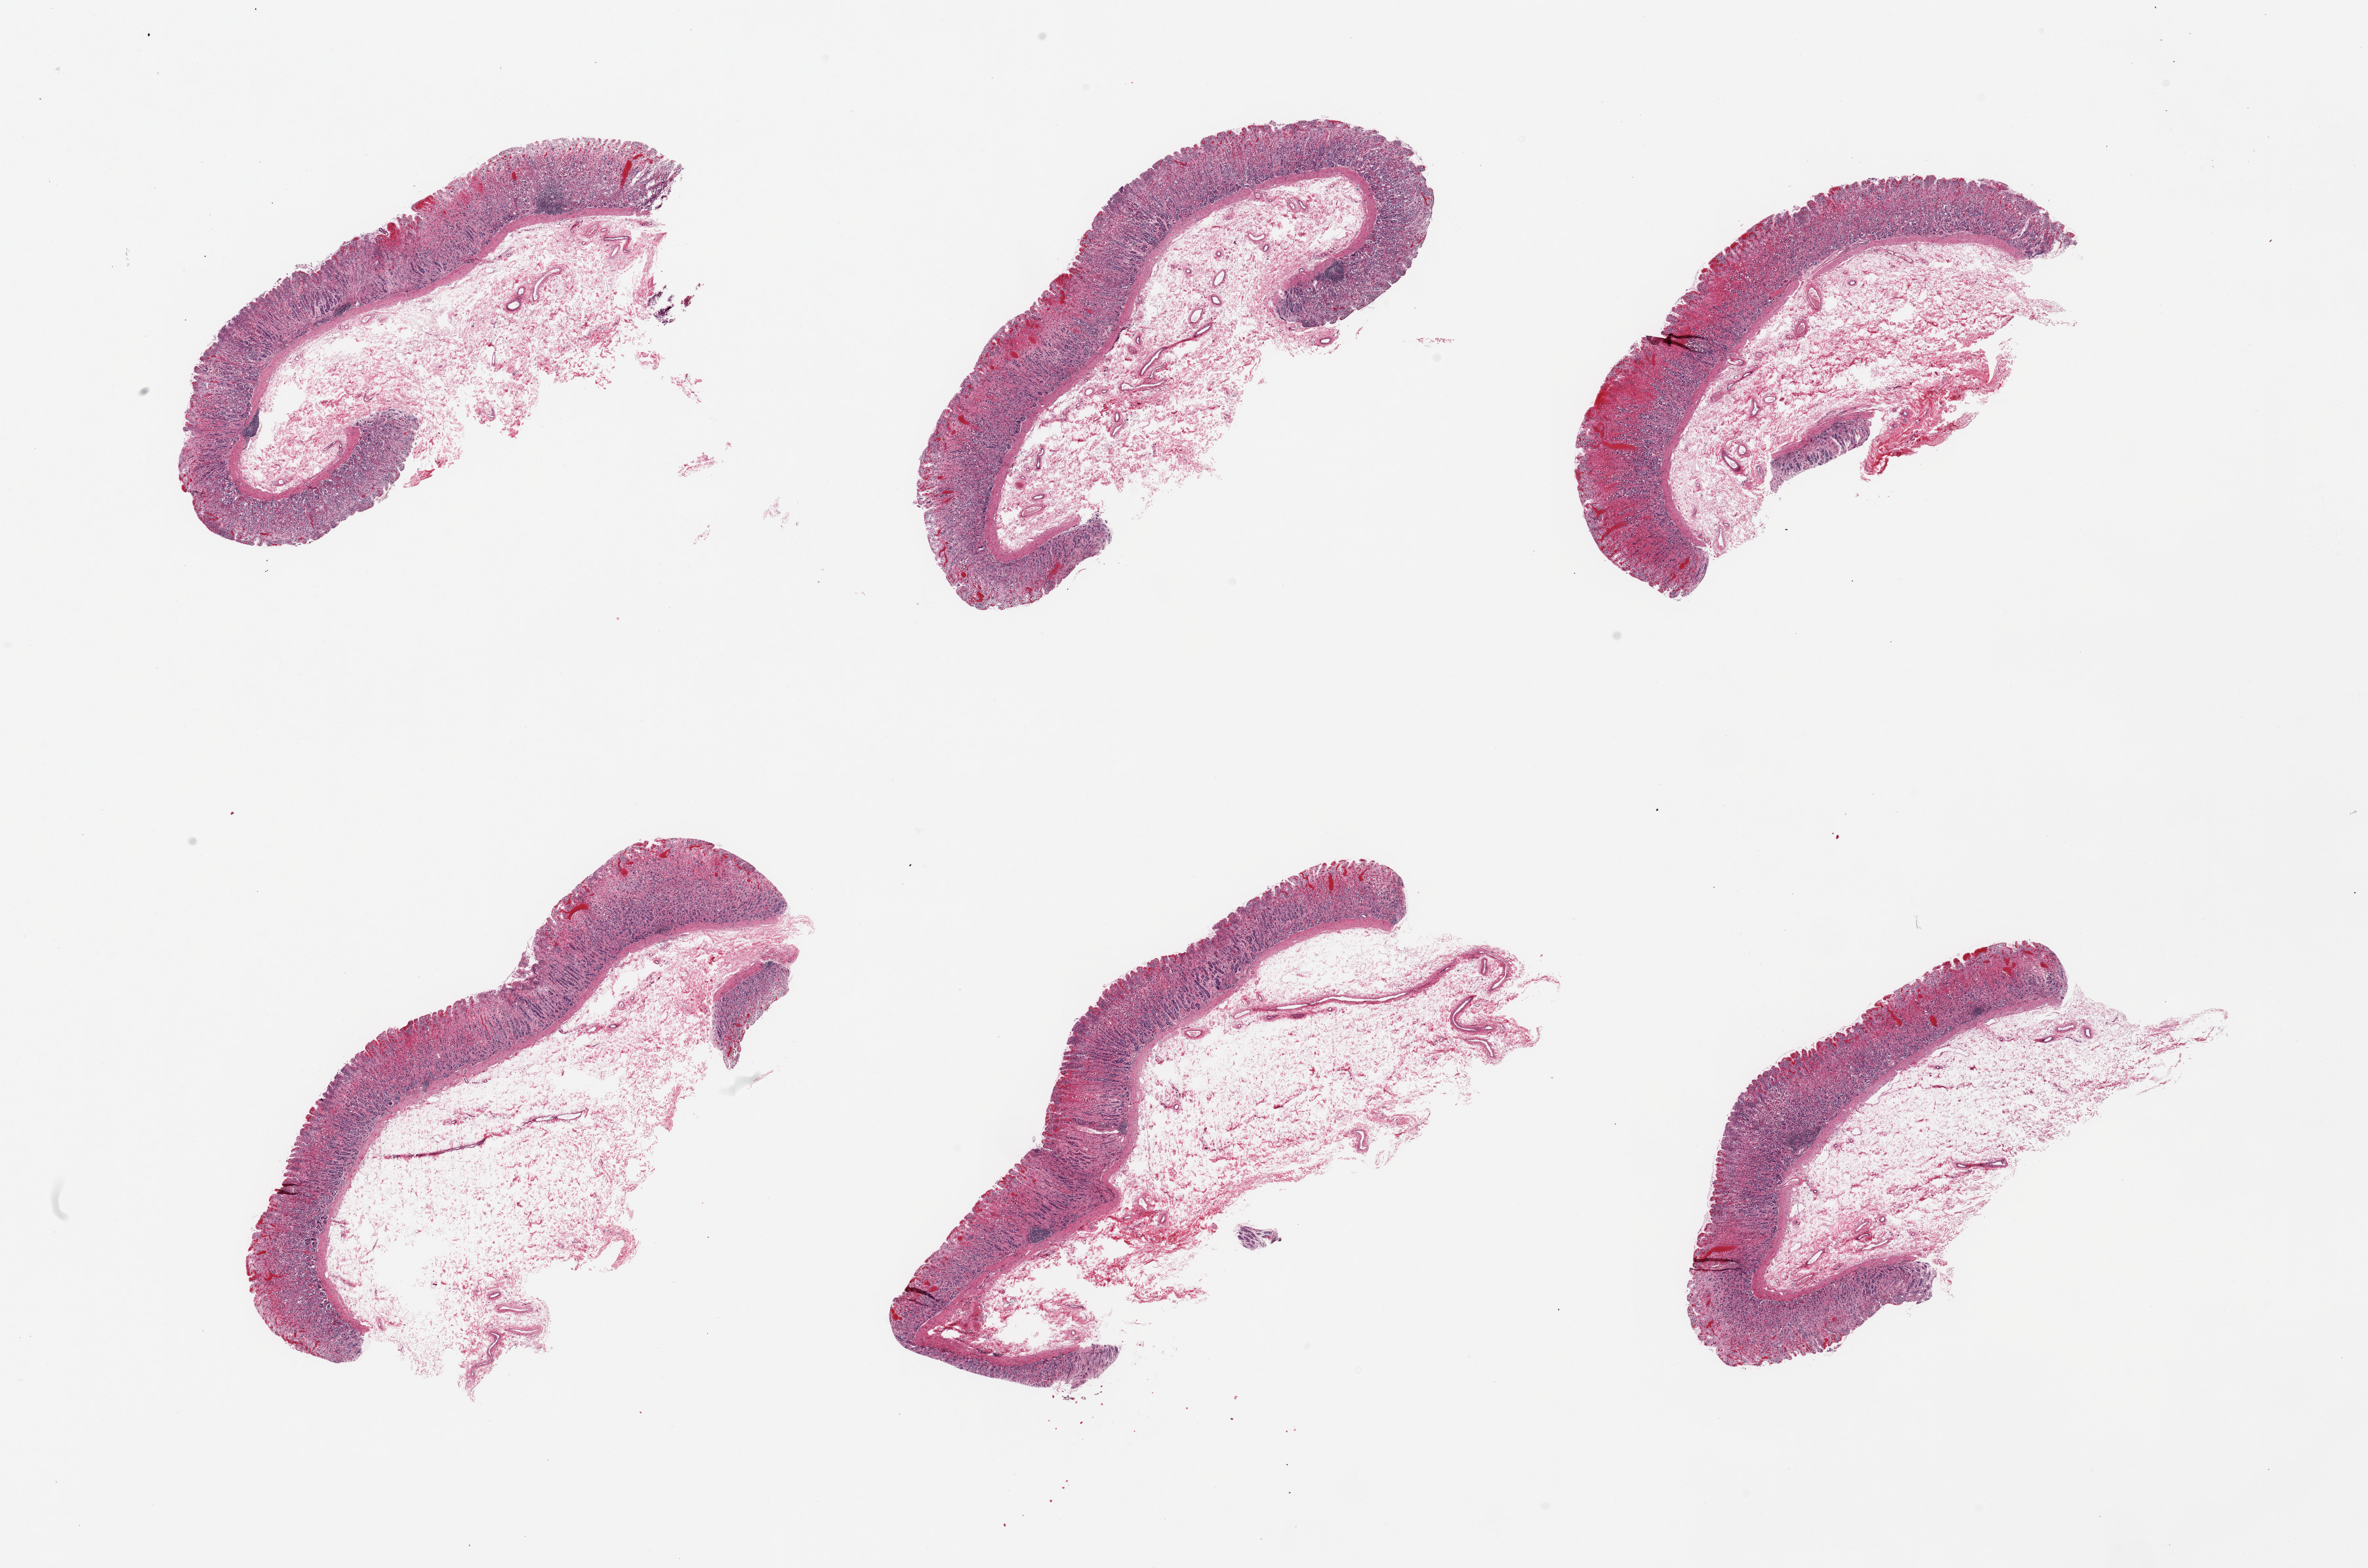
Whole-slide image, H&E stain, whole scanned area (about 28.5 x 18.9 mm) shown as a low-resolution overview. PAXgene-fixed, paraffin-embedded tissue. Sampled site (target tissue): stomach. Tissue donor sample. Donor: female.
* review note (as recorded): 6 pieces; mucosa and submucosa only, congestion and hemorrhage